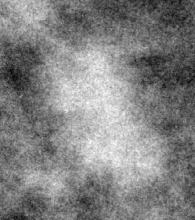
Cropped region of a digitized screen-film mammogram centred on a radiologist-marked abnormality, right breast, CC view, BI-RADS breast density category 1 (scale 1–4).
Mass, shape irregular, margins ill defined; BI-RADS assessment category 4; pathology result (as recorded, not read from the image): malignant.